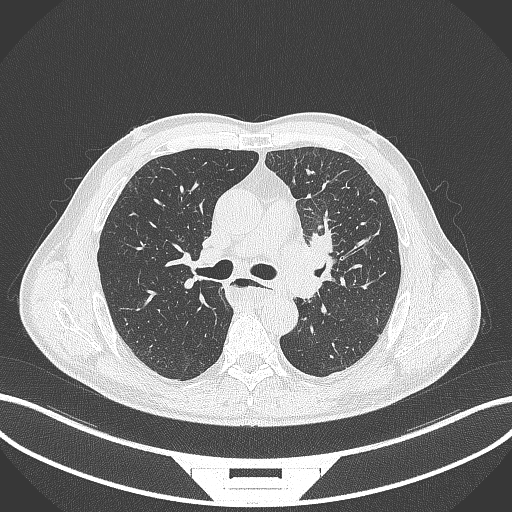
Chest CT, one axial slice; slice 234 of 411 in the series (ordered by position); reconstruction kernel B70f; lung window (W 1500 / L -600 HU); 1 mm slice thickness; 512 × 512 image matrix, field of view 400 × 400 mm. Patient: male, 57 years. Case-level facts recorded for this patient, not image findings: clinical TNM (as recorded): T2a N1 M0.
Structures marked on this image (rectangle marked by the reading radiologist):
- lung tumour (recorded histology: squamous cell carcinoma): bounding box (x1, y1, x2, y2) in pixels: (278, 228, 347, 304)